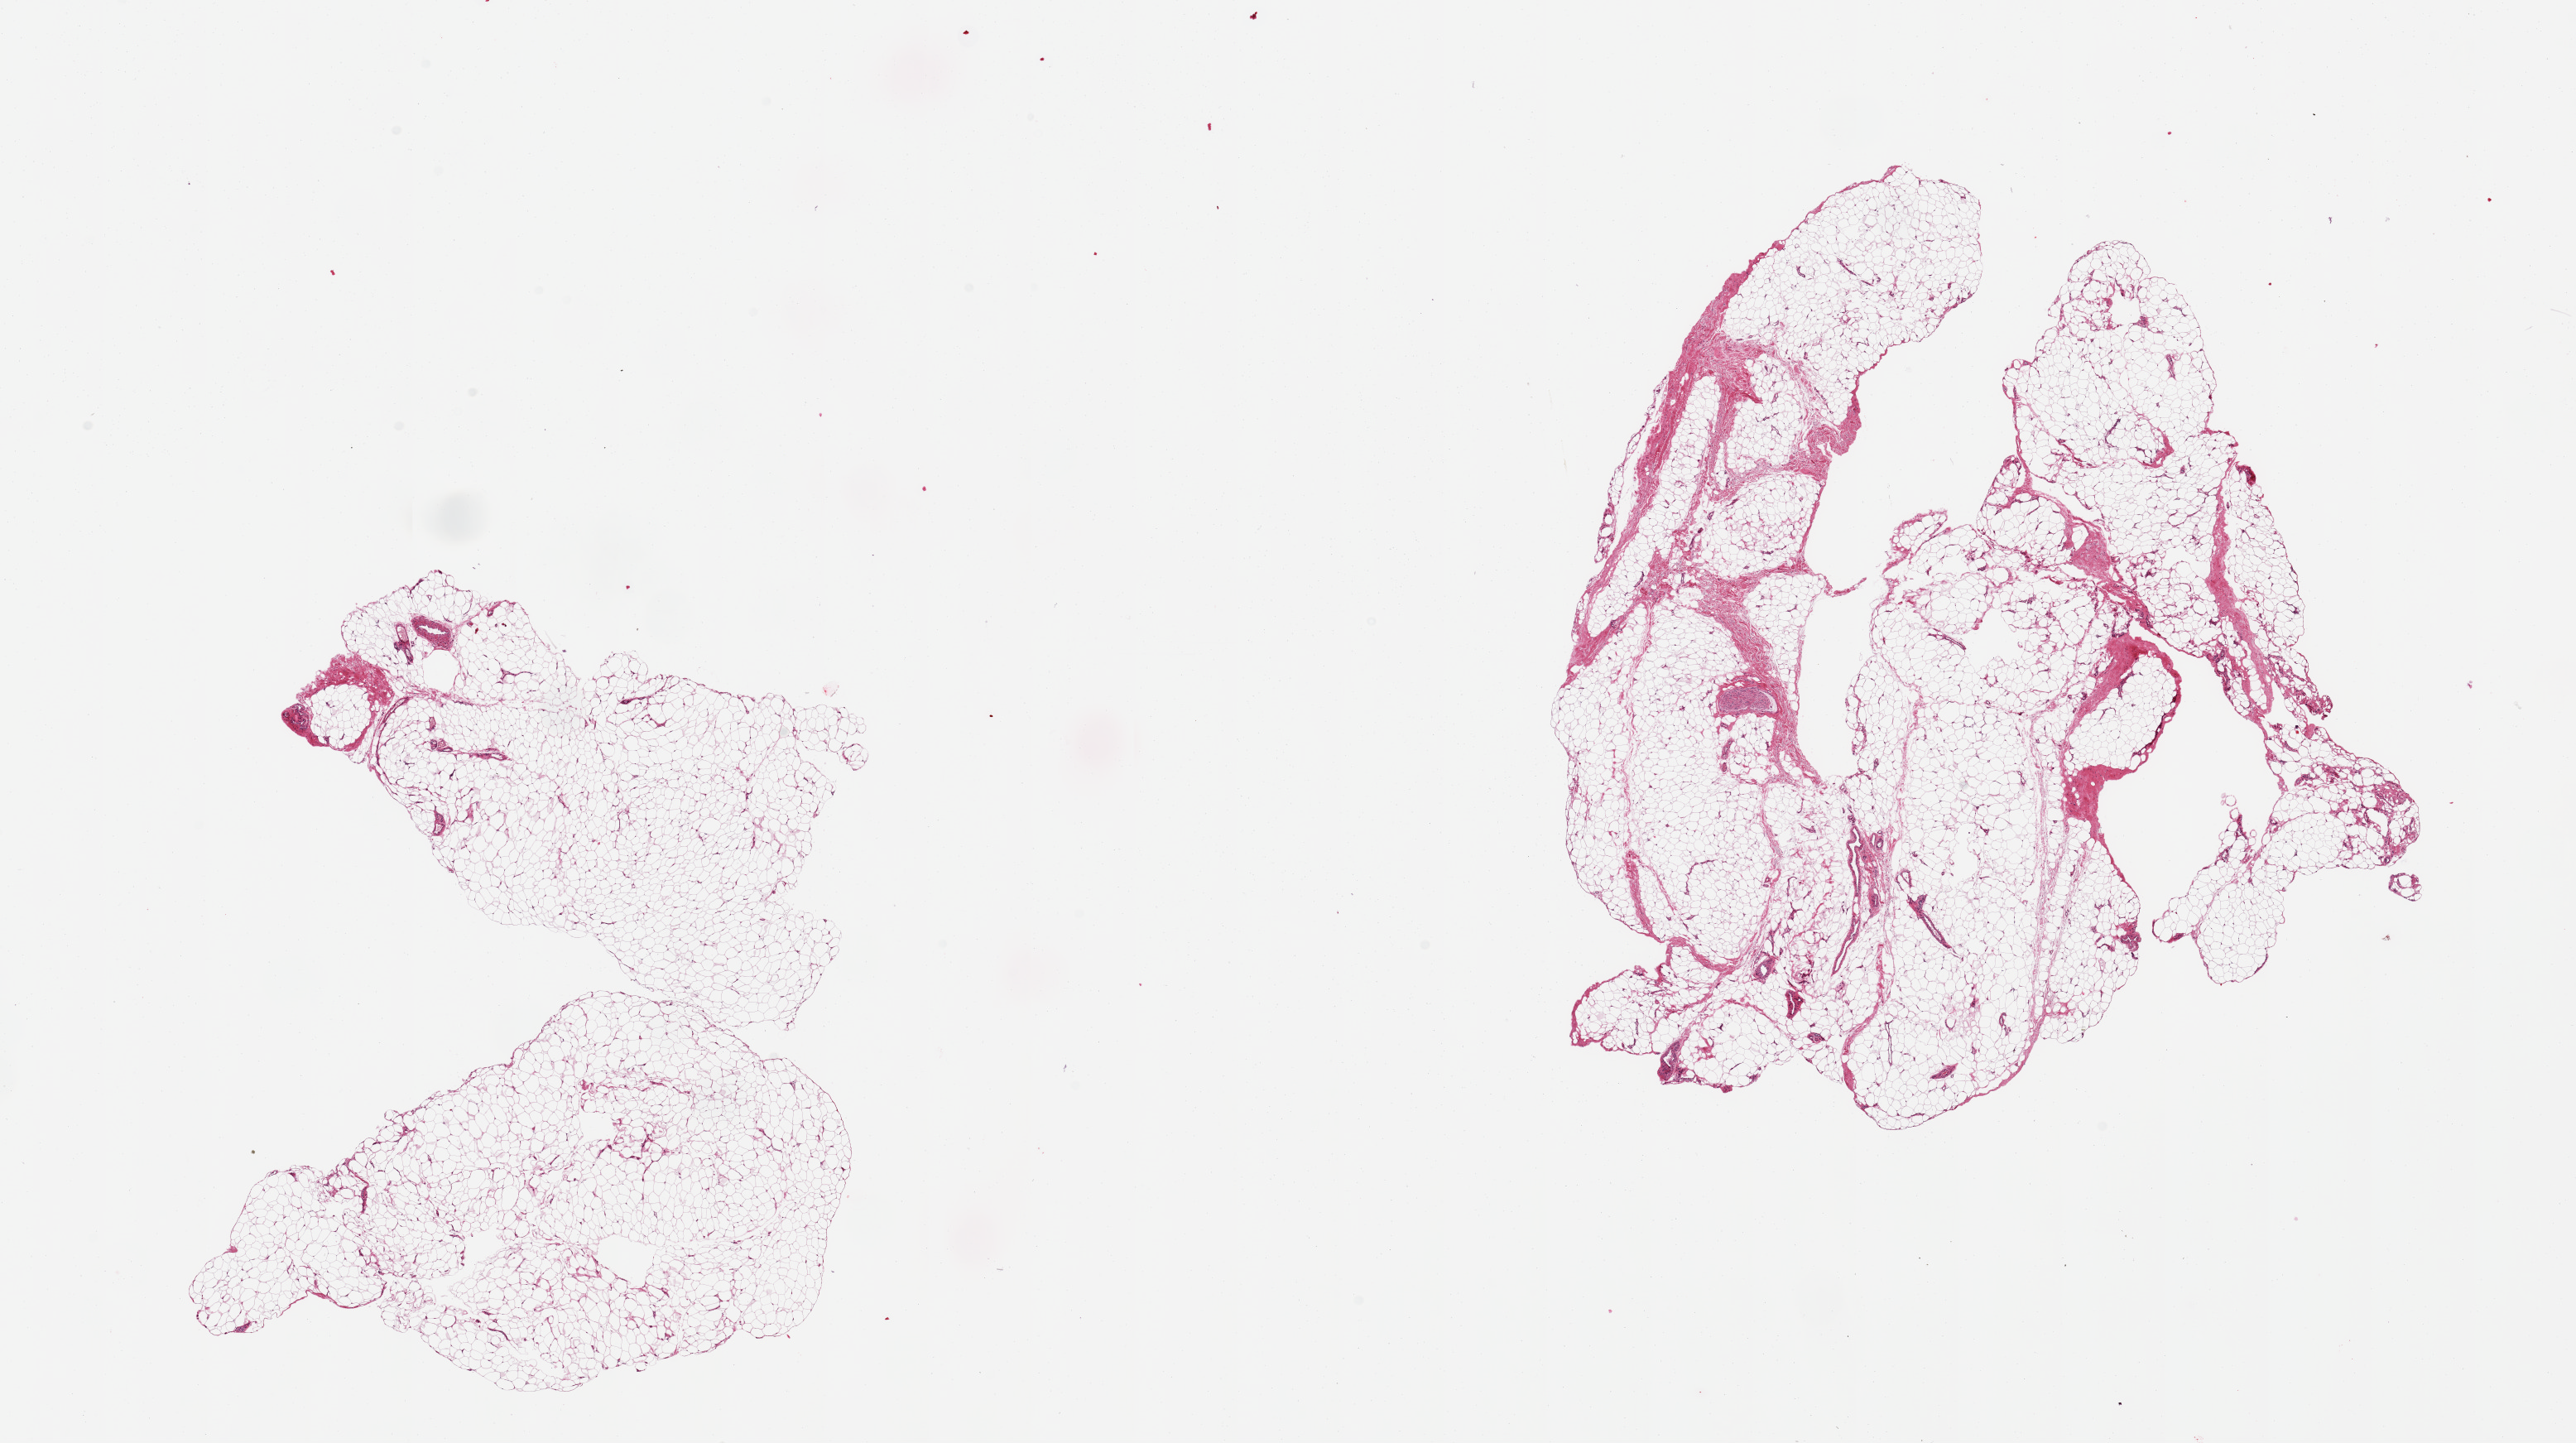
H&E whole-slide image, brightfield — whole scanned area (about 24.6 x 13.8 mm, slide scanned at 20x) shown as a low-resolution overview. PAXgene-fixed paraffin-embedded (PFPE) section. Sampled site (target tissue): adipose tissue. Tissue donor sample. Donor: male.
- pathologist's review note for this sample: 2 pieces; fascia/vascular elements are ~10% of tissue